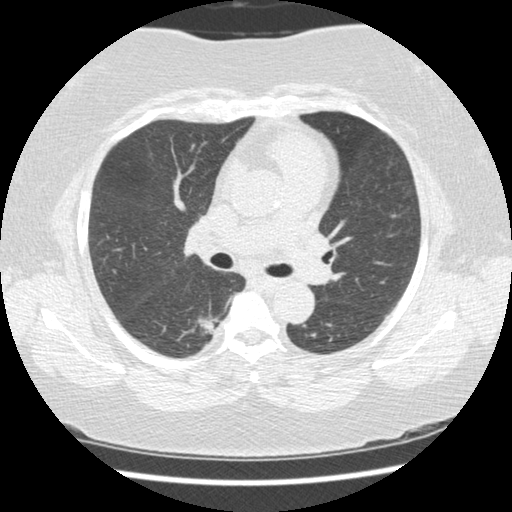
Chest CT (low-dose screening protocol), one axial image. Second annual screen. Lung window (W 1500 / L -600 HU). 1.25 mm slice thickness. Female, age 58 years at enrolment. Current smoker at enrolment.
Expert-annotated lung lesion, bounding box (x1, y1, x2, y2) in pixels: (189, 309, 228, 349). The exam's reader record, not a measurement of the box and not confirmed to be the same lesion: non-calcified nodule or mass ≥4 mm, right lower lobe, 15 × 15 mm, spiculated (stellate) margins, soft tissue attenuation, pre-existing on the prior screen: yes; interval growth: yes. Official screen result: positive, change unspecified: nodule(s) >= 4 mm or enlarging nodule(s), mass(es), or other non-specific abnormalities suspicious for lung cancer. Participant outcome: lung cancer diagnosed 21 days after this screen — adenocarcinoma, NOS, right lower lobe, stage IB (AJCC 6th edition), 15 mm at pathology.